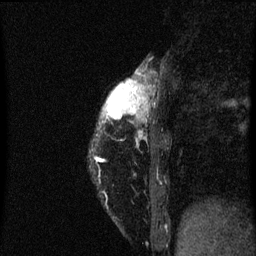
Breast MRI (dynamic contrast-enhanced), one sagittal slice. Dynamic contrast-enhanced series, image 2 of 3 at this slice position (ordered by acquisition). 1.5 T. TE 4.2 ms, TR 8 ms. 2 mm slice thickness. 256 × 256 image matrix. Female patient, age 38 years.
Structures marked on this image (semi-automatically segmented with operator editing):
- analysis volume of interest (the breast-tissue region the enhancement analysis was run in; not a lesion): bounding box <96,74,151,151> (left, top, right, bottom; pixels)
- tumour enhancement mask (voxels above the 70 % enhancement threshold inside the analysis volume of interest): <104,80,147,119>